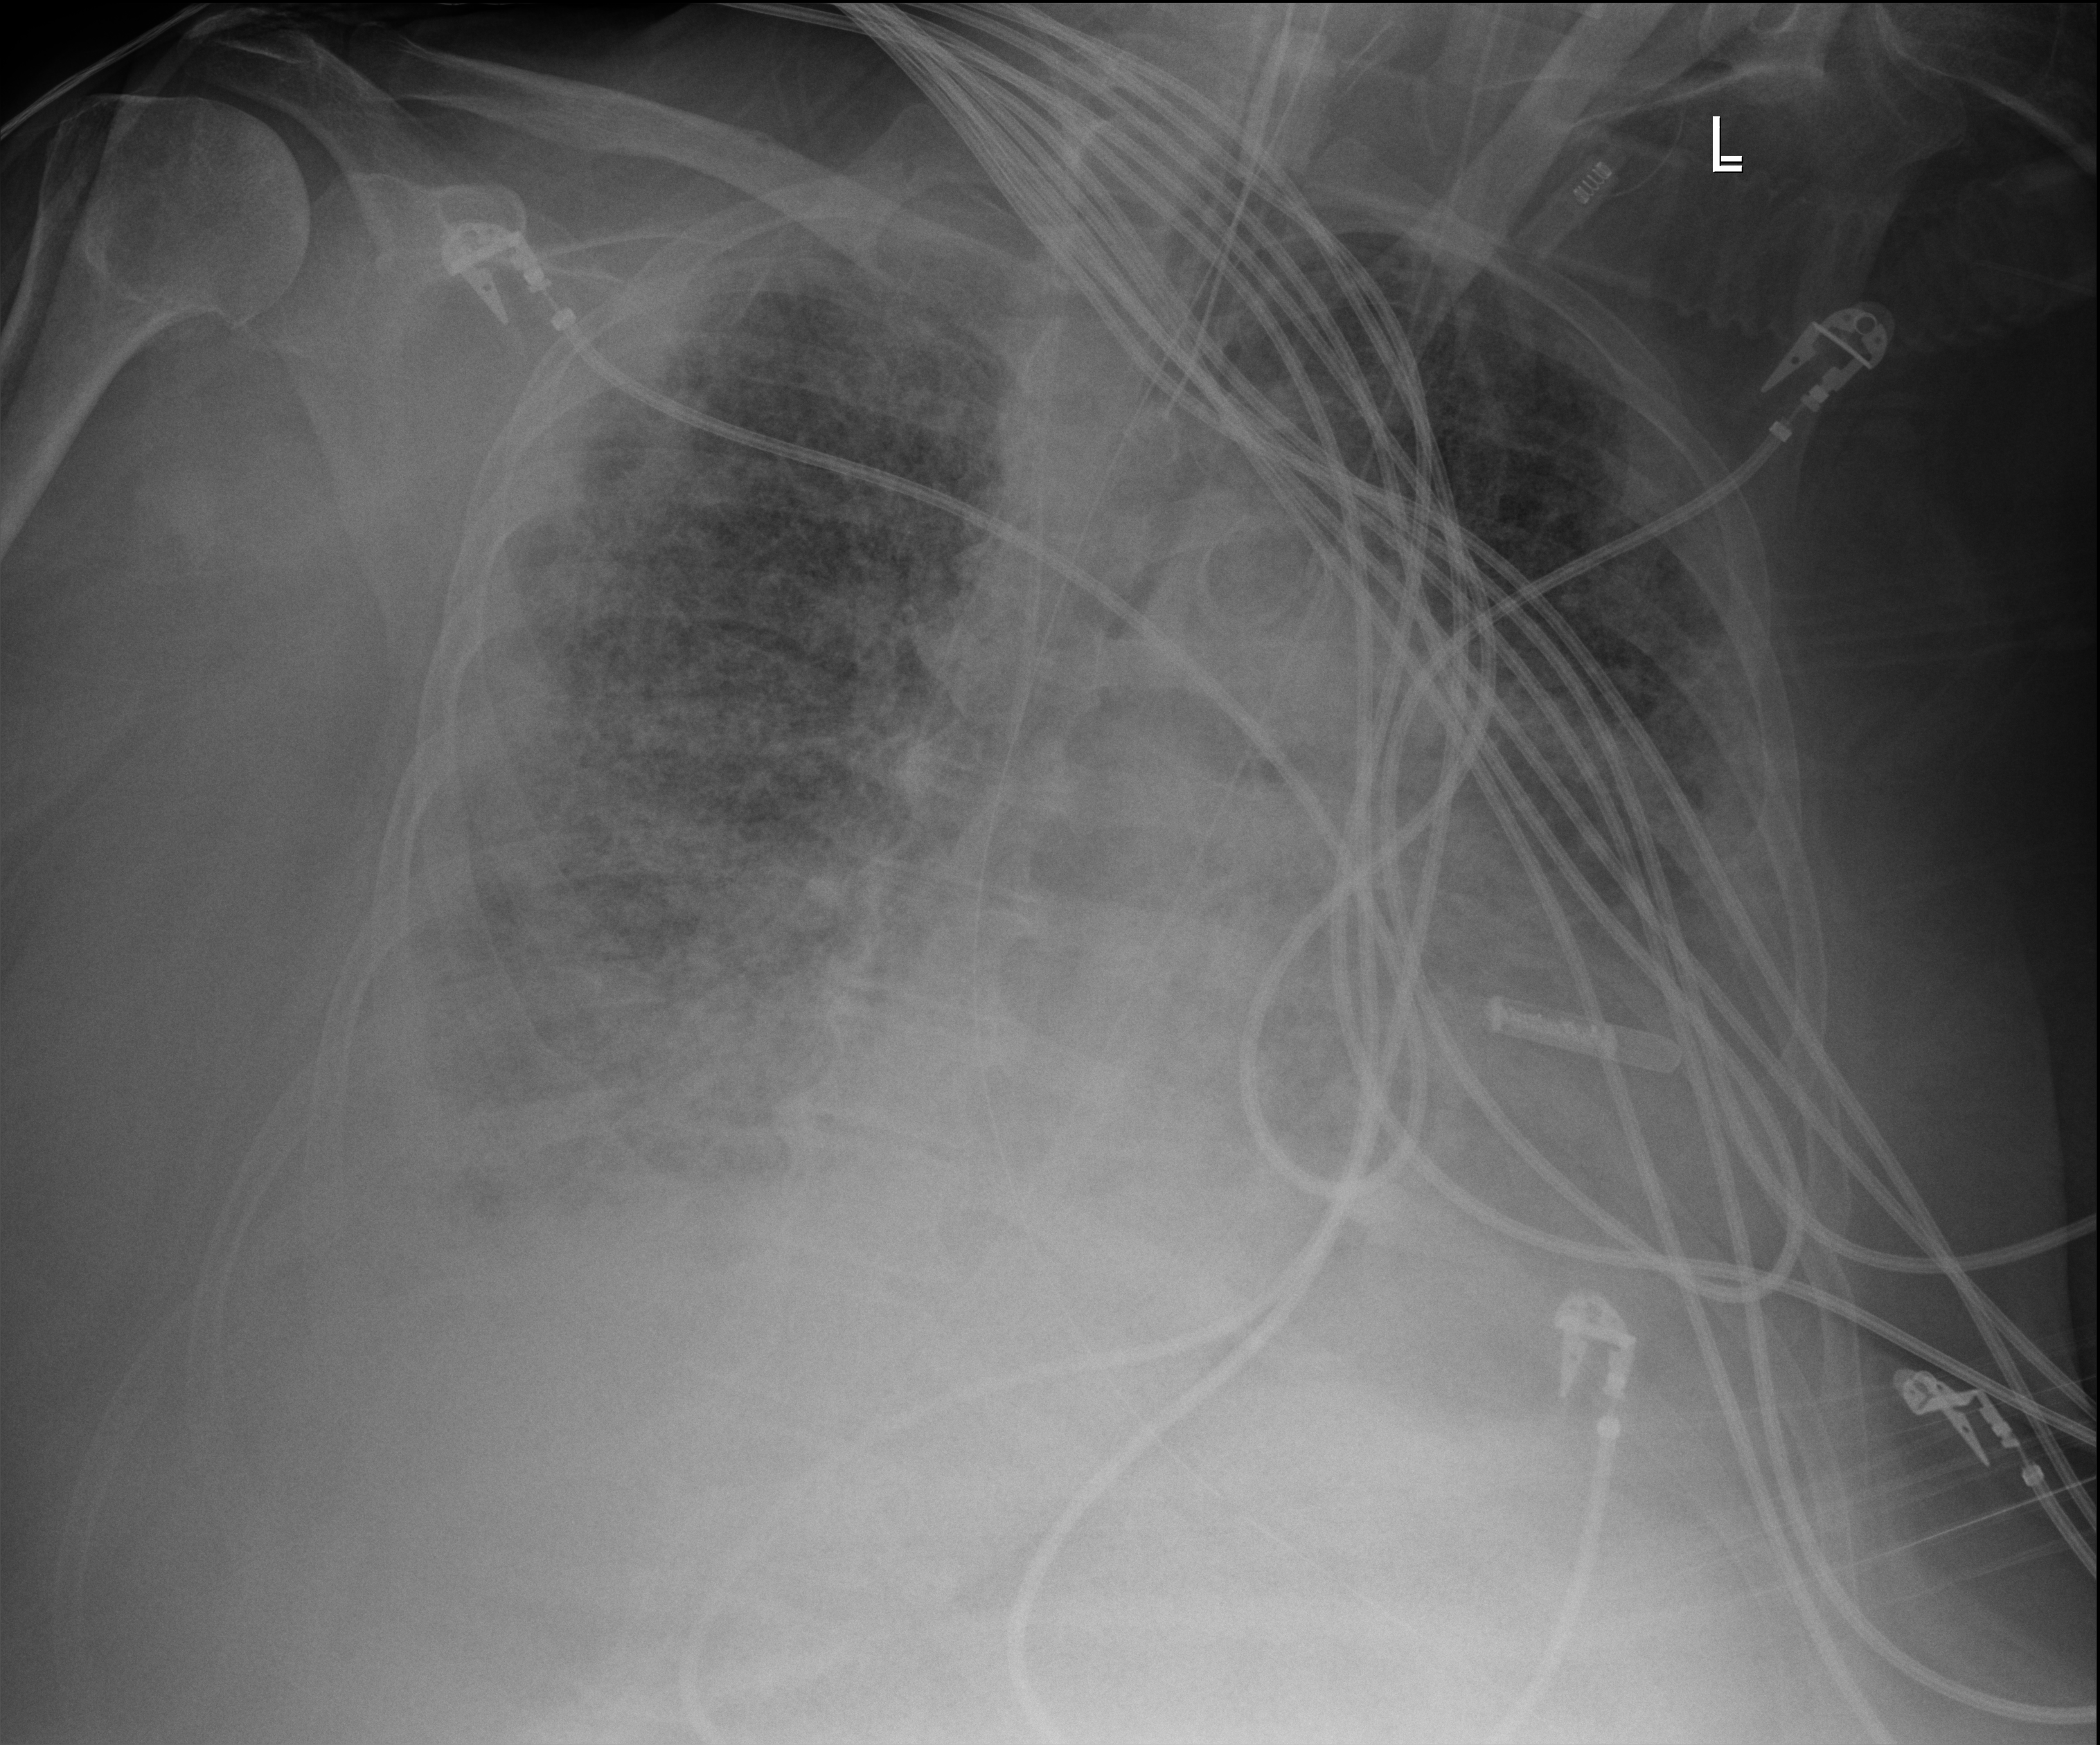
Bedside chest radiograph (digital radiography); anteroposterior (AP) projection. Patient hospitalised with COVID-19; female, aged 60–74 years.
Hospital-stay facts (about this admission, not read from this image; timing relative to this image not recorded): length of hospital stay: 28 days.